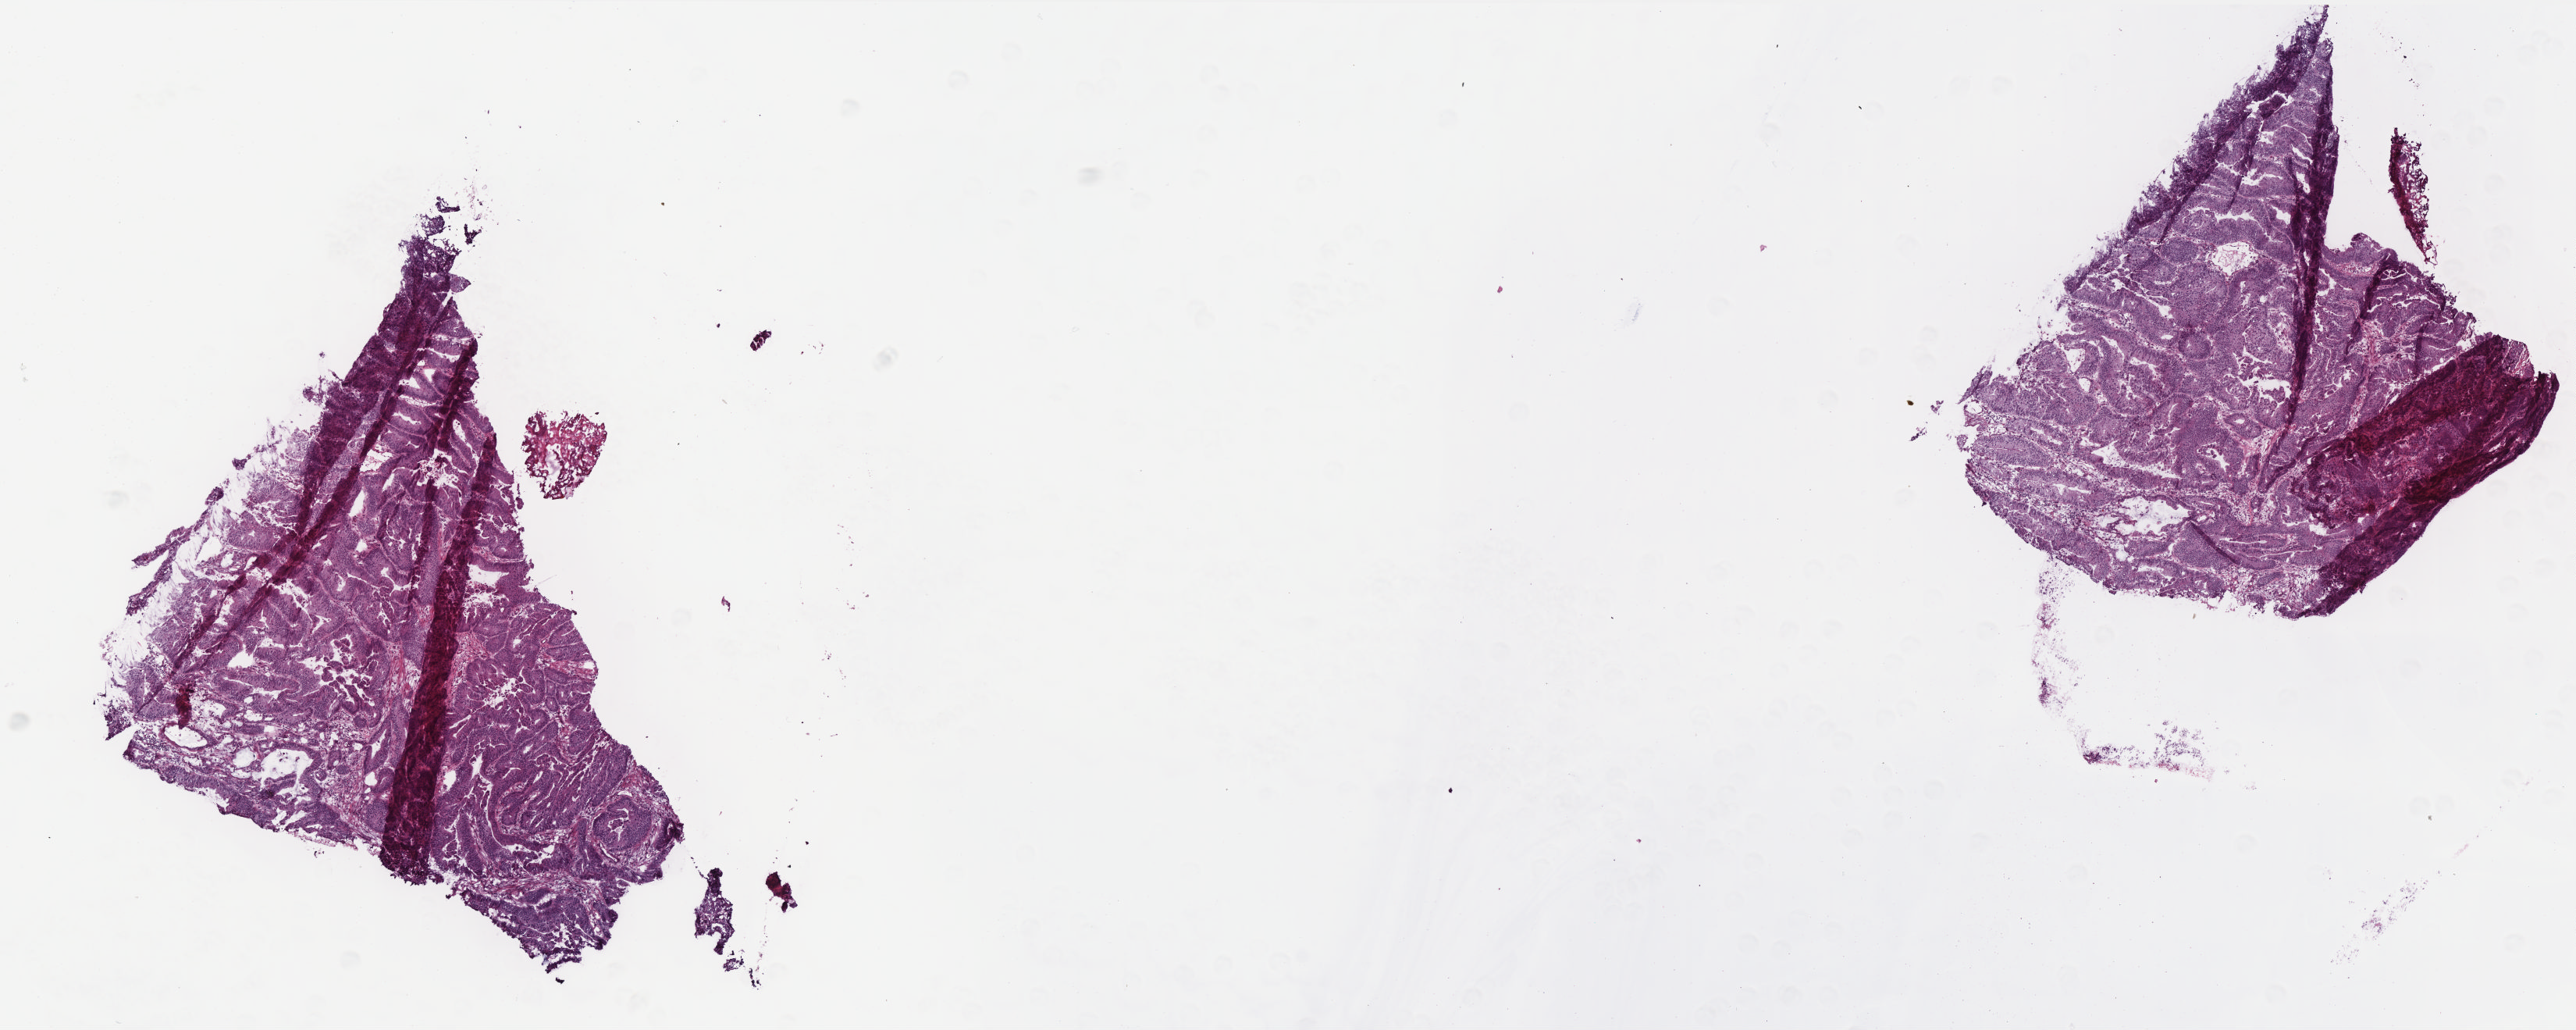
H&E-stained whole-slide image — whole scanned area (about 13.2 x 5.3 mm, slide scanned at 40x) shown as a low-resolution overview. Frozen section from the bottom of the tissue portion. Sample: primary tumour, colon. Male, age 68 years at initial diagnosis. Pathologist review of this section (percent, as recorded): tumour cells 95%, tumour nuclei 95%, normal cells 0%, stromal cells 4%, necrosis 1%. Infiltration values recorded for this section: lymphocyte infiltration 2%, monocyte infiltration 1%, neutrophil infiltration 0%.
• AJCC pathologic stage: II (5th edition)
• TNM: T3 N0 M0
• diagnosis: Adenocarcinoma, NOS (ascending colon)
• lymph nodes positive (case pathology): 0 of 12 examined